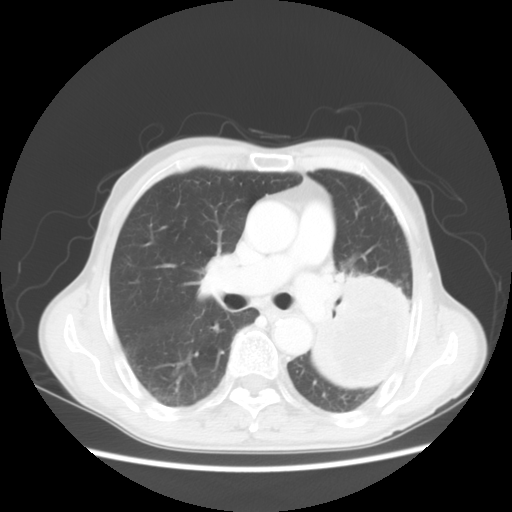
Chest CT, one axial slice. Position 30 of 51 along the scan axis. Lung window (W 1500 / L -600 HU). 5 mm slice thickness. 512 × 512 image matrix. Patient: male, 64 years. From the clinical record (not read from this slice): clinical TNM (as recorded): T4 N0 M0; histopathological grade: G2-3.
Structures marked on this image (rectangle marked by the reading radiologist):
- lung tumour (recorded histology: squamous cell carcinoma): bounding box <310,277,419,395> (left, top, right, bottom; pixels)